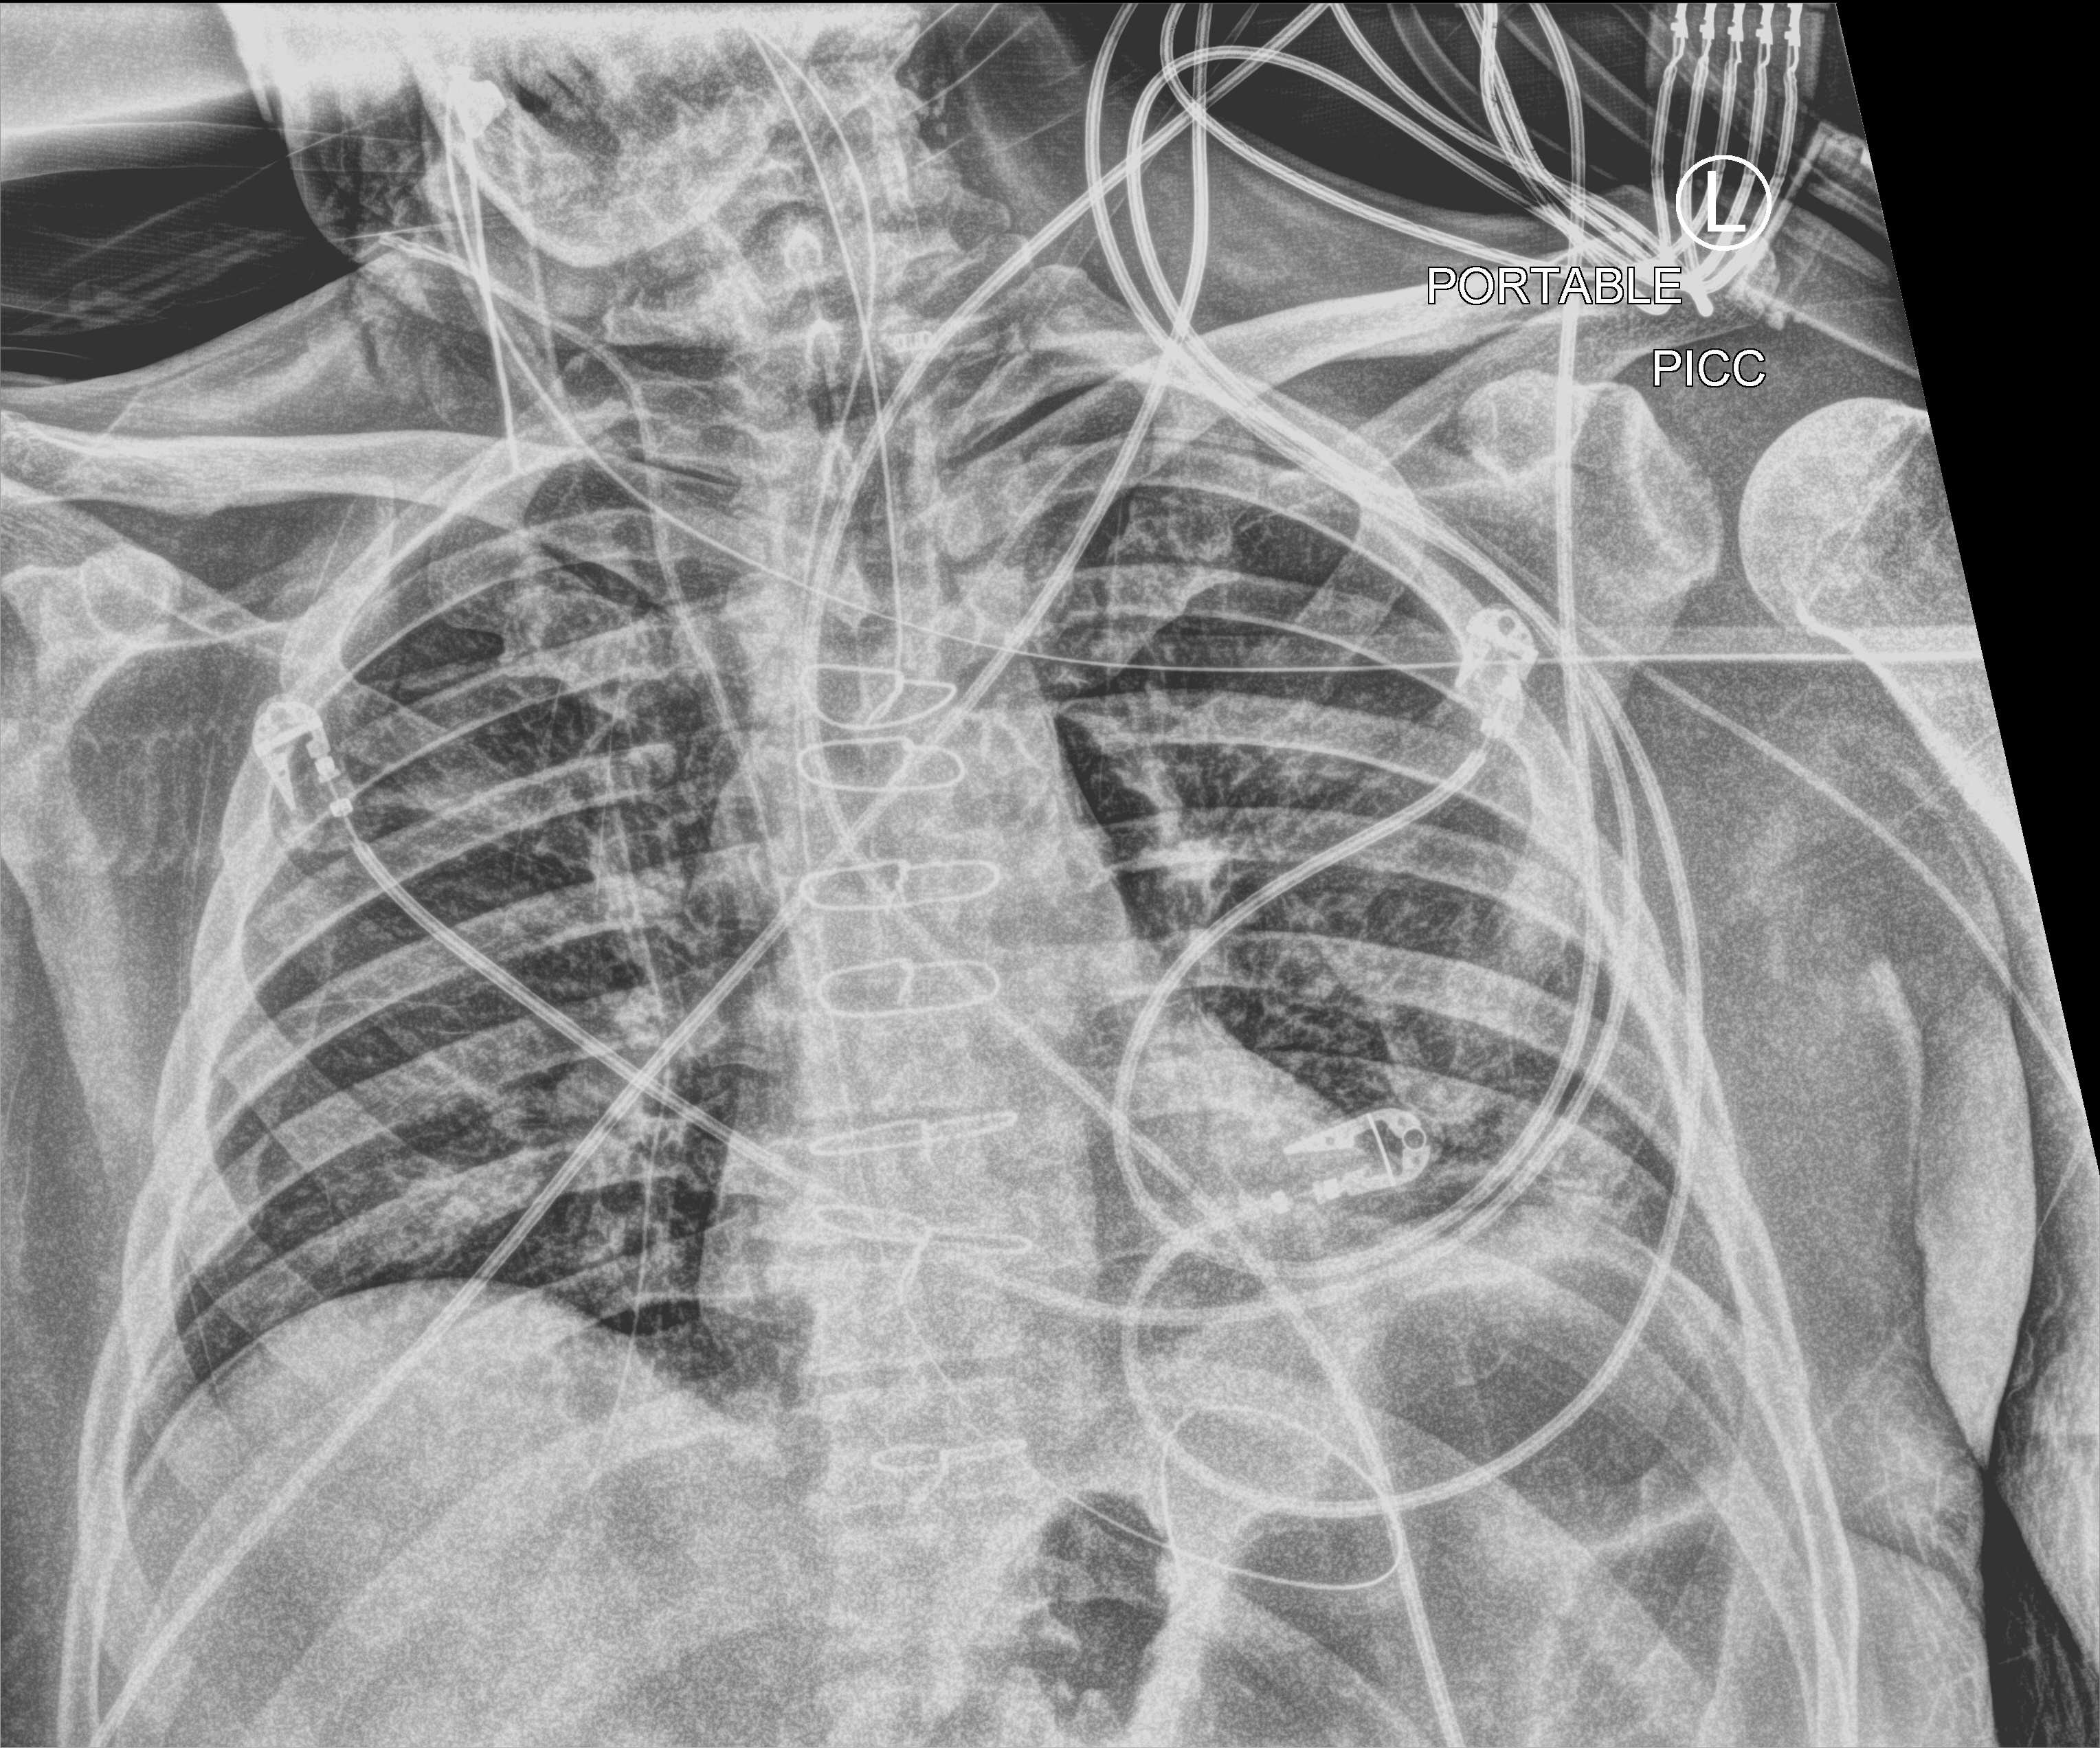
Bedside chest radiograph (computed radiography), anteroposterior (AP) projection. Male patient hospitalised with COVID-19, age 60–74 years.
Hospital-stay facts (about this admission, not read from this image; timing relative to this image not recorded):
- length of hospital stay: 44 days